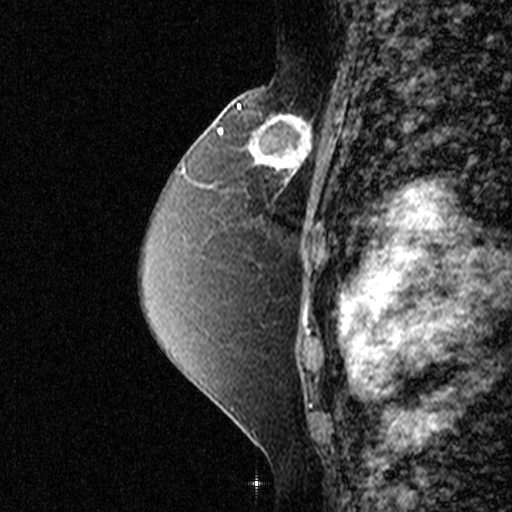
Breast MRI (dynamic contrast-enhanced), one sagittal slice. Position 28 of 44 along the scan axis. Dynamic contrast-enhanced study with each time point stored as its own series, time point 2 of 3 at this slice position (early post-contrast, ordered by acquisition time). 1.5 T. TE 4.5 ms, TR 11 ms. 3 mm slice thickness. 512 × 512 image matrix. Patient: female, 49 years. Case-level facts recorded for this patient, not image findings: setting: breast cancer imaged before/during neoadjuvant chemotherapy; receptor status: triple-negative.
Structures marked on this image (semi-automatically segmented with operator editing):
- analysis volume of interest (the breast-tissue region the enhancement analysis was run in; not a lesion): bounding box <244,100,335,197> (left, top, right, bottom; pixels)
- tumour enhancement mask (voxels above the 90 % enhancement threshold inside the analysis volume of interest): <252,112,313,193>